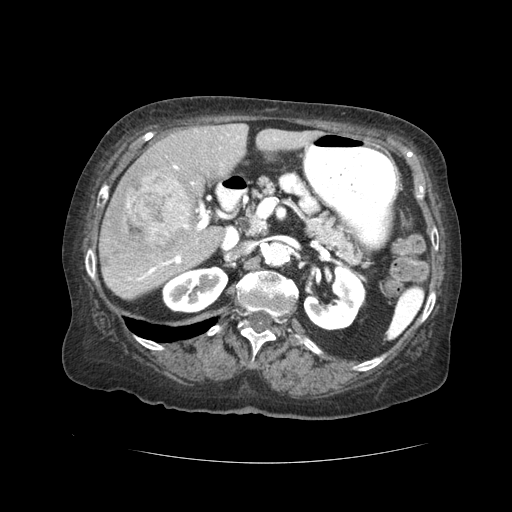
Contrast-enhanced abdominal CT (liver protocol), one axial slice. Slice 16 of 59 in the series (ordered by position). Soft-tissue window (W 400 / L 40 HU). 2.5 mm slice thickness. 512 × 512 image matrix. Case-level facts recorded for this patient, not image findings: diagnosis: hepatocellular carcinoma (patient treated with transarterial chemoembolisation; whether this scan precedes or follows treatment is not stated here); TNM stage (as recorded): Stage-I; Child-Pugh class: A.
Outlined on this slice (semi-automatically segmented with operator editing):
- liver parenchyma outside the tumour (the mass and vessels are separate outlines, so this box may not span the whole liver): box from (x=98, y=124) to (x=318, y=300) px
- mass: (x=111, y=173)–(x=193, y=244)
- liver vessels: (x=128, y=136)–(x=276, y=281)